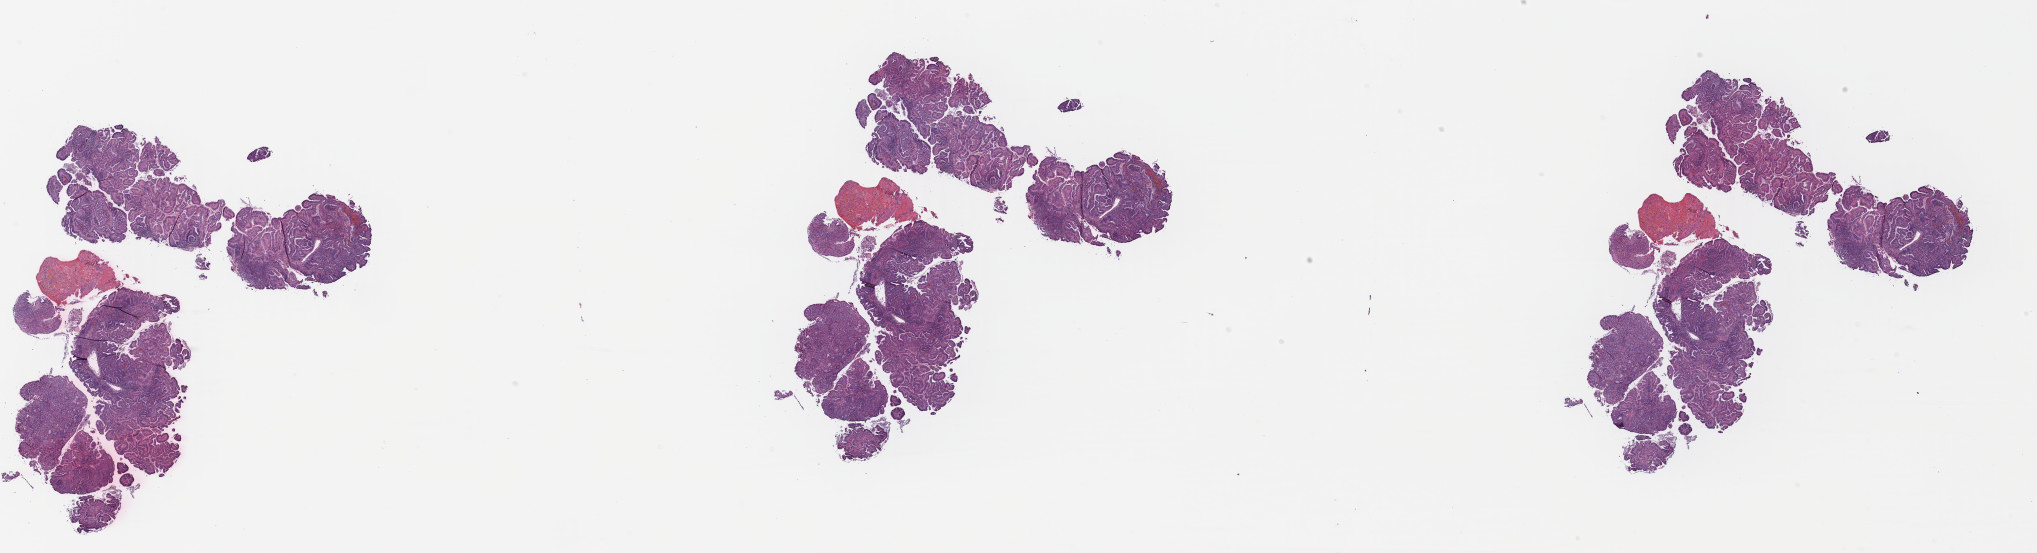
Hematoxylin and eosin (H&E) stained whole-slide image — whole scanned area (about 32.0 x 8.7 mm, acquisition: 40x scan) shown as a low-resolution overview. FFPE section. Primary tumour sample from the uterus. Female patient; age at initial diagnosis 34 years. Histologic grade: G2 (moderately differentiated).
• pathologic diagnosis: Endometrioid adenocarcinoma, NOS (endometrium)
• FIGO stage: II